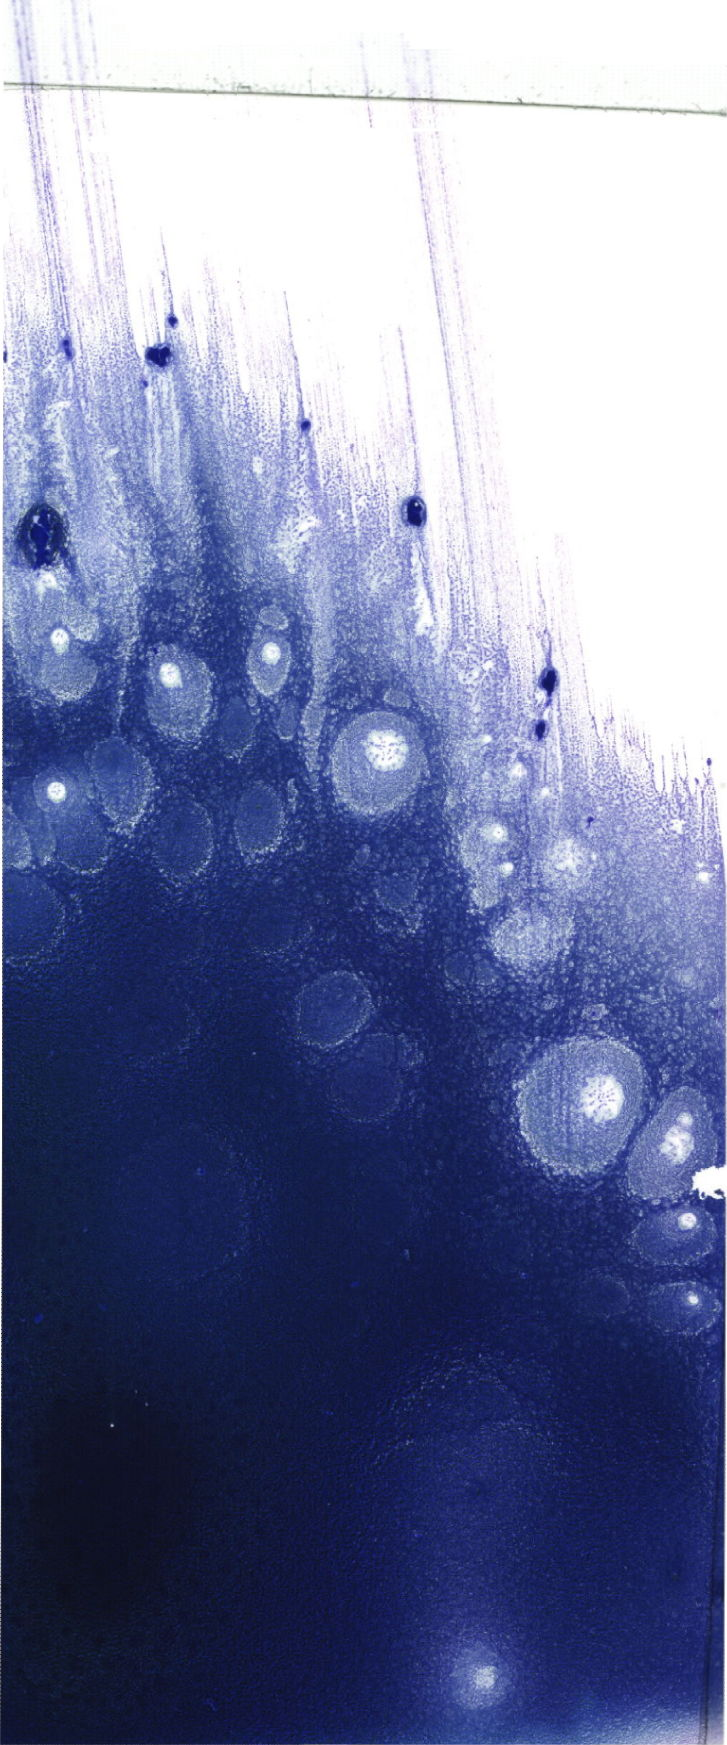
Bone marrow aspirate smear, May-Grünwald-Giemsa (MGG) stain, whole-slide image, low-resolution overview of the scanned area, about 20.6 x 49.5 mm. Female patient.
Diagnosis: B Acute Lymphoblastic Leukemia.